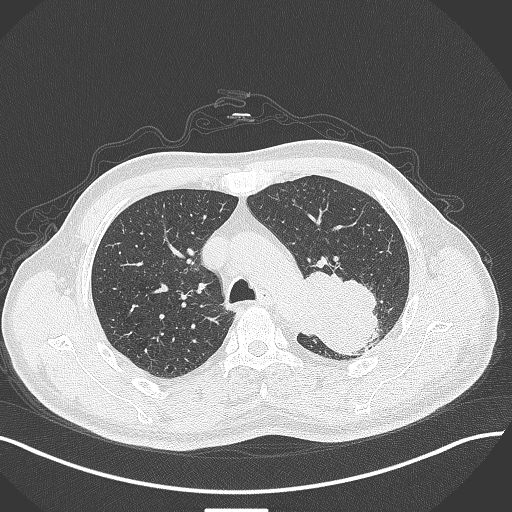
Chest CT, one axial slice; position 308 of 429 along the scan axis; reconstruction kernel B70f; lung window (W 1500 / L -600 HU); 512 × 512 image matrix, field of view 400 × 400 mm. Patient: male, 55 years. From the clinical record (not read from this slice): clinical TNM (as recorded): T3 N0 M1c; histopathological grade: G3.
Outlined on this slice (bounding box drawn by a radiologist):
- lung tumour (recorded histology: adenocarcinoma): bounding box (x1, y1, x2, y2) in pixels: (295, 268, 383, 356)